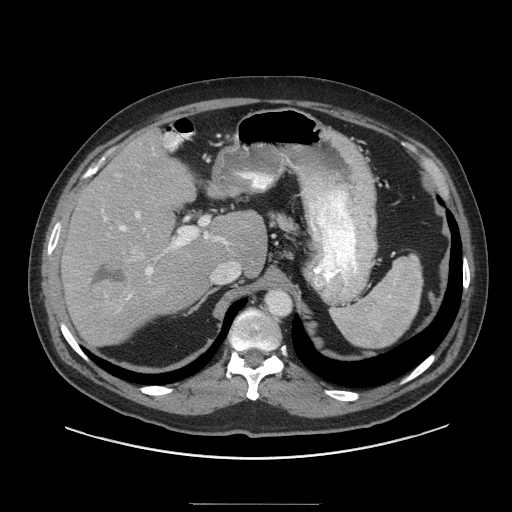
Contrast-enhanced abdominal CT (liver protocol), one axial slice; slice 64 of 91 in the series (ordered by position); reconstruction kernel STANDARD; 140 kVp; soft-tissue window (W 400 / L 40 HU); 2.5 mm slice thickness; 512 × 512 image matrix, field of view 440 × 440 mm. Case-level facts recorded for this patient, not image findings: diagnosis: hepatocellular carcinoma (patient treated with transarterial chemoembolisation; whether this scan precedes or follows treatment is not stated here); TNM stage (as recorded): Stage-I; Child-Pugh class: A.
Annotated regions visible in this slice (semi-automatic segmentation, software-assisted and operator-edited):
- liver parenchyma outside the tumour (the mass and vessels are separate outlines, so this box may not span the whole liver): bounding box <60,136,266,346> (left, top, right, bottom; pixels)
- mass: <88,260,134,311>
- liver vessels: <104,211,239,298>